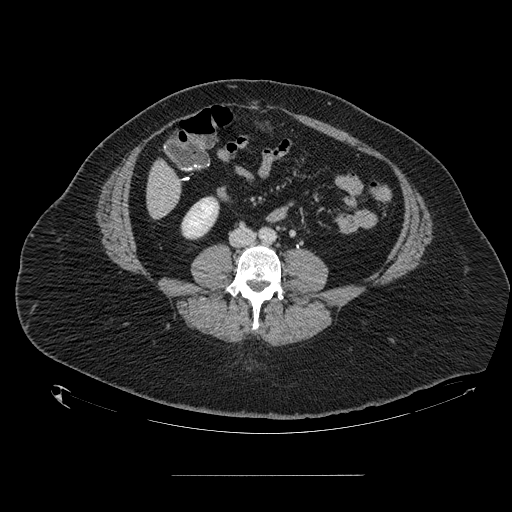
Contrast-enhanced abdominal CT, one axial slice. Position 18 of 164 along the scan axis. 120 kVp. Intravenous contrast given. Soft-tissue window (W 400 / L 40 HU). 2.5 mm slice thickness. 512 × 512 image matrix, field of view 495 × 495 mm. Female patient, age 52 years. Case-level facts recorded for this patient, not image findings: diagnosis: colorectal cancer liver metastases, imaged before liver resection; multiple liver metastases: yes; largest metastasis: 3.5 cm; disease in both lobes: no.
Outlined on this slice (outlined manually by an expert reader):
- liver: bounding box [x1, y1, x2, y2] px = [148, 162, 180, 217]